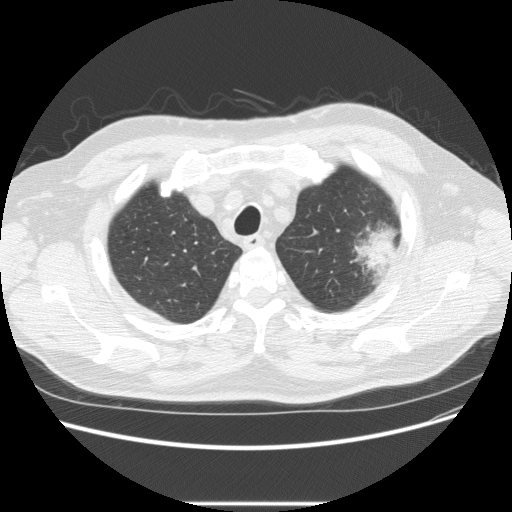
Low-dose screening chest CT, axial slice. Baseline annual screen. Lung window (W 1500 / L -600 HU). 2.5 mm slice thickness. Standard (soft-tissue) reconstruction kernel (STANDARD). Slice 43 of 233 in the series. Male, age 73 years at enrolment.
Lesion marked by an expert reader, bounding box (x1, y1, x2, y2) in pixels: (332, 216, 408, 283). The screening reader recorded 2 non-calcified nodules or masses ≥4 mm on this exam (left upper lobe, right upper lobe); which of them this box marks is not recorded. Official screen result: positive, change unspecified: nodule(s) >= 4 mm or enlarging nodule(s), mass(es), or other non-specific abnormalities suspicious for lung cancer. Lung cancer was diagnosed 11 days after this screen: bronchiolo-alveolar adenocarcinoma, NOS, other location, well differentiated (G1), stage IV (AJCC 6th edition).